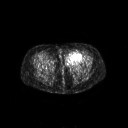
FDG PET of an extremity soft-tissue mass (from a PET/CT study), one axial slice. Position 34 of 267 along the scan axis. 3.27 mm slice thickness. 128 × 128 image matrix. Female patient, age 47 years. From the clinical record (not read from this slice): histological type: myxofibrosarcoma; grade: intermediate; site of the primary tumour: left thigh.
Structures marked on this image (expert contour drawn on MRI and transferred to this co-registered scan by the dataset authors):
- gross tumour volume including surrounding oedema: box from (x=66, y=51) to (x=83, y=65) px
- gross tumour volume (mass): (x=66, y=51)–(x=82, y=62)